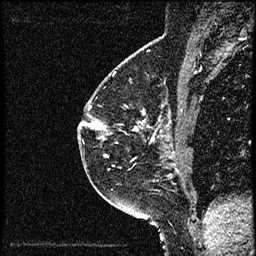
Breast MRI (dynamic contrast-enhanced), one sagittal slice. Slice 37 of 52 in the series (ordered by position). Dynamic contrast-enhanced study with each time point stored as its own series, time point 2 of 3 at this slice position (early post-contrast, ordered by acquisition time). 1.5 T. TE 4.2 ms, TR 17.6 ms. 256 × 256 image matrix. Female patient, age 49 years. Case-level facts recorded for this patient, not image findings: setting: breast cancer imaged before/during neoadjuvant chemotherapy; receptor status: HER2-positive.
Structures marked on this image (semi-automatic segmentation, software-assisted and operator-edited):
- analysis volume of interest (the breast-tissue region the enhancement analysis was run in; not a lesion): bounding box <85,65,182,175> (left, top, right, bottom; pixels)
- tumour enhancement mask (voxels above the 100 % enhancement threshold inside the analysis volume of interest): <89,106,172,158>